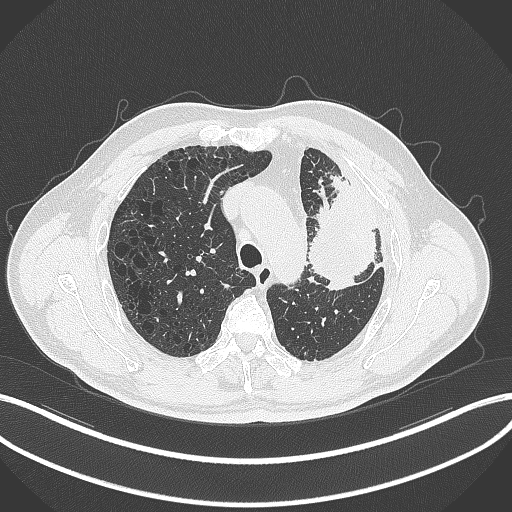
Chest CT, one axial slice. Slice 233 of 297 in the series (ordered by position). Reconstruction kernel B70f. Lung window (W 1500 / L -600 HU). 512 × 512 image matrix. Male patient, age 68 years. From the clinical record (not read from this slice): clinical TNM (as recorded): T3 N3 M1.
Annotated regions visible in this slice (bounding box drawn by a radiologist):
- lung tumour (recorded histology: adenocarcinoma): bounding box <297,157,383,300> (left, top, right, bottom; pixels)